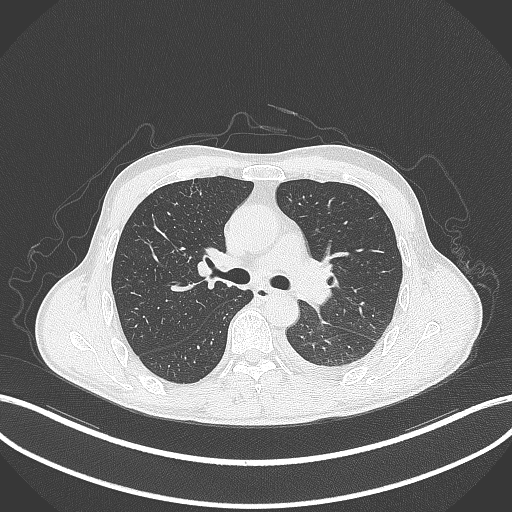
Chest CT, one axial slice; position 206 of 295 along the scan axis; reconstruction kernel B70f; lung window (W 1500 / L -600 HU); 512 × 512 image matrix, field of view 400 × 400 mm. Male patient, age 47 years. Case-level facts recorded for this patient, not image findings: clinical TNM (as recorded): T3 N1 M1c; histopathological grade: G3.
Outlined on this slice (bounding box drawn by a radiologist):
- lung tumour (recorded histology: small cell carcinoma): bounding box (x1, y1, x2, y2) in pixels: (300, 282, 332, 304)